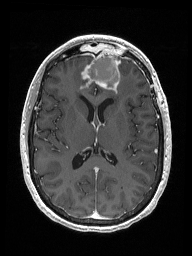
Brain MRI from a brain-tumour surgery series, one axial slice. Position 78 of 192 along the scan axis. T1-weighted post-contrast. 192 × 256 image matrix. Case-level facts recorded for this patient, not image findings: histopathology: Metastastic Carcinoma from Breast primary.
Structures marked on this image (manually delineated by an expert):
- previous resection cavity: box from (x=87, y=52) to (x=120, y=87) px